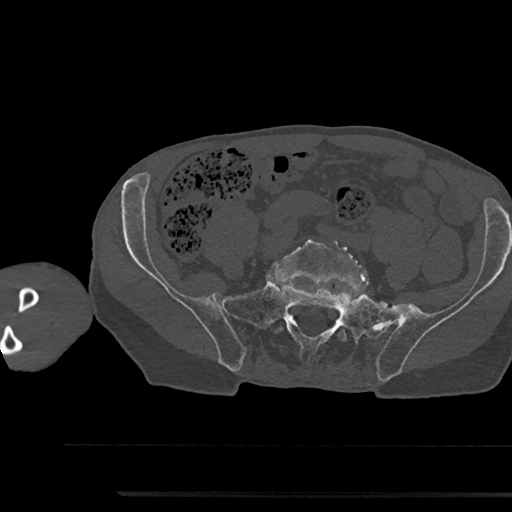
CT including the spine, one axial slice; slice 311 of 797 in the series (ordered by position); reconstruction kernel Br40s/3; bone window (W 1800 / L 400 HU); 512 × 512 image matrix, field of view 367 × 367 mm. Patient: male, 79 years. Case-level facts recorded for this patient, not image findings: primary cancer: prostate.
Annotated regions visible in this slice (semi-automatic segmentation, software-assisted and operator-edited):
- L5 vertebra: box from (x=274, y=235) to (x=369, y=341) px